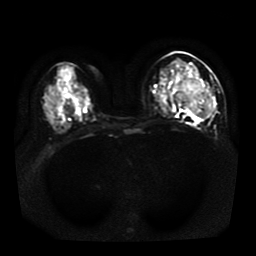
Breast MRI, one axial slice. Slice 22 of 41 in the series (ordered by position). Diffusion-weighted series; image 2 of 4 stored at this slice position (different b-values; order by instance number). 1.5 T. 256 × 256 image matrix, field of view 330 × 330 mm. Female patient.
Structures marked on this image (expert manual segmentation):
- tumour on diffusion-weighted imaging: box from (x=176, y=80) to (x=213, y=115) px